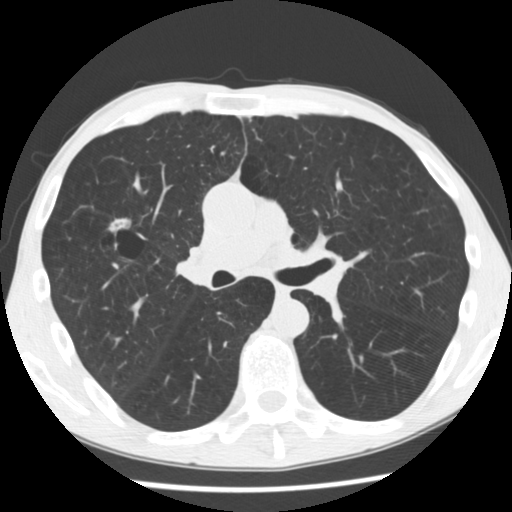
Axial slice from a low-dose chest CT screening exam, baseline annual screen, lung window (W 1500 / L -600 HU), 120 kVp, slice 127 of 292 in the series. Male participant, aged 56 years at enrolment. Current smoker at enrolment.
Lesion marked by an expert reader, bounding box [x1, y1, x2, y2] px = [97, 206, 152, 254]. The screening reader recorded 2 non-calcified nodules or masses ≥4 mm on this exam (right upper lobe, right upper lobe); which of them this box marks is not recorded. Official screen result: positive, change unspecified: nodule(s) >= 4 mm or enlarging nodule(s), mass(es), or other non-specific abnormalities suspicious for lung cancer. Participant outcome: lung cancer diagnosed 476 days after this screen — squamous cell carcinoma, NOS, right upper lobe, right middle lobe, well differentiated (G1), stage IA (AJCC 6th edition), 27 mm at pathology.